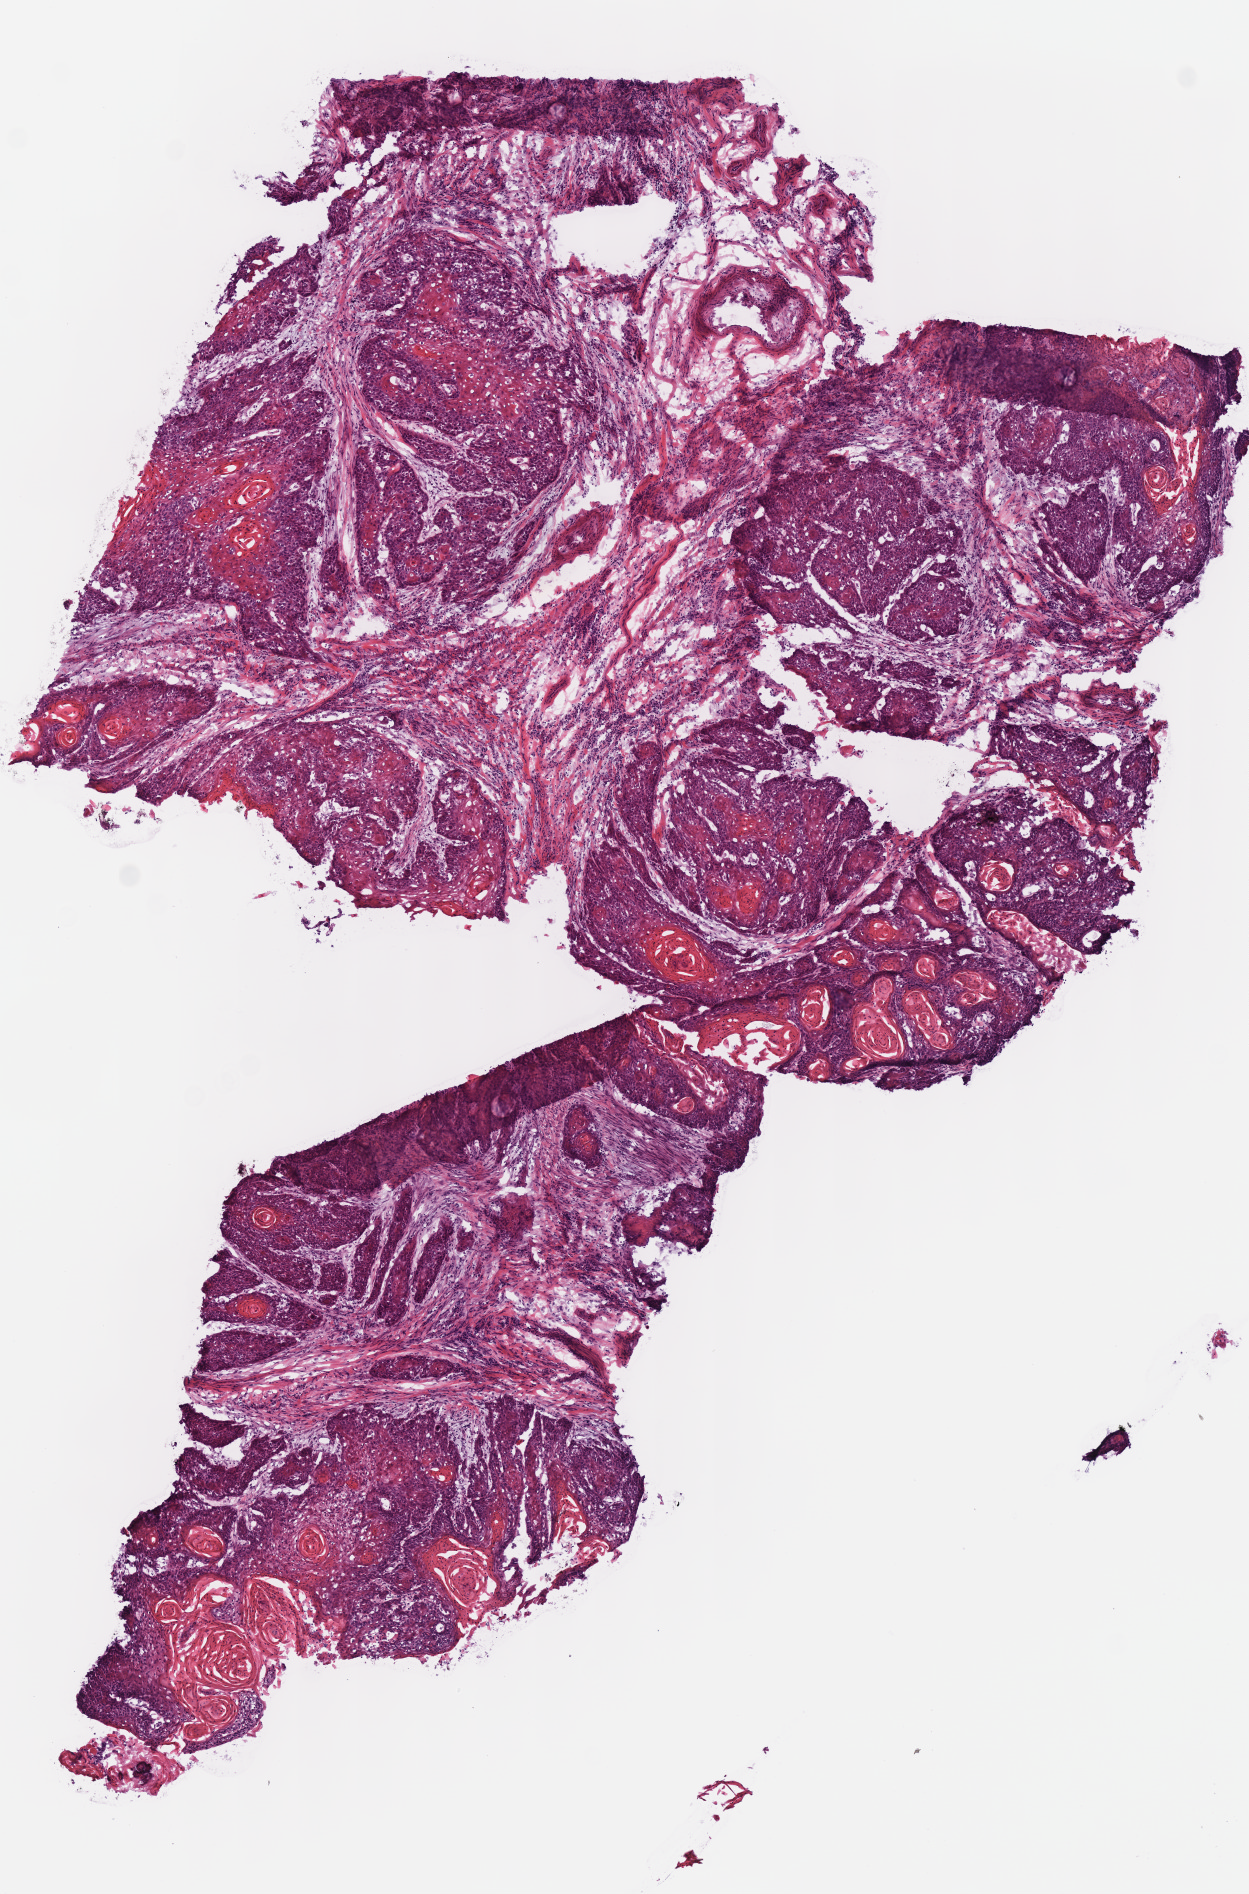
Hematoxylin and eosin (H&E) stained whole-slide image — whole scanned area (about 4.9 x 7.5 mm) shown as a low-resolution overview; frozen section from the bottom of the tissue portion; sample: primary tumour, head and neck. Male, age 47 years at initial diagnosis. Histologic grade: G2 (moderately differentiated). Pathologist review of this section (percent, as recorded): tumour cells 100%, tumour nuclei 80%, normal cells 0%, stromal cells 0%, necrosis 0%. Infiltration values recorded for this section: lymphocyte infiltration 10%, monocyte infiltration 0%, neutrophil infiltration 0%.
AJCC pathologic stage: IVA (7th edition). TNM: T4a N2b. Histologic diagnosis: Squamous cell carcinoma, NOS (overlapping lesion of lip, oral cavity and pharynx).